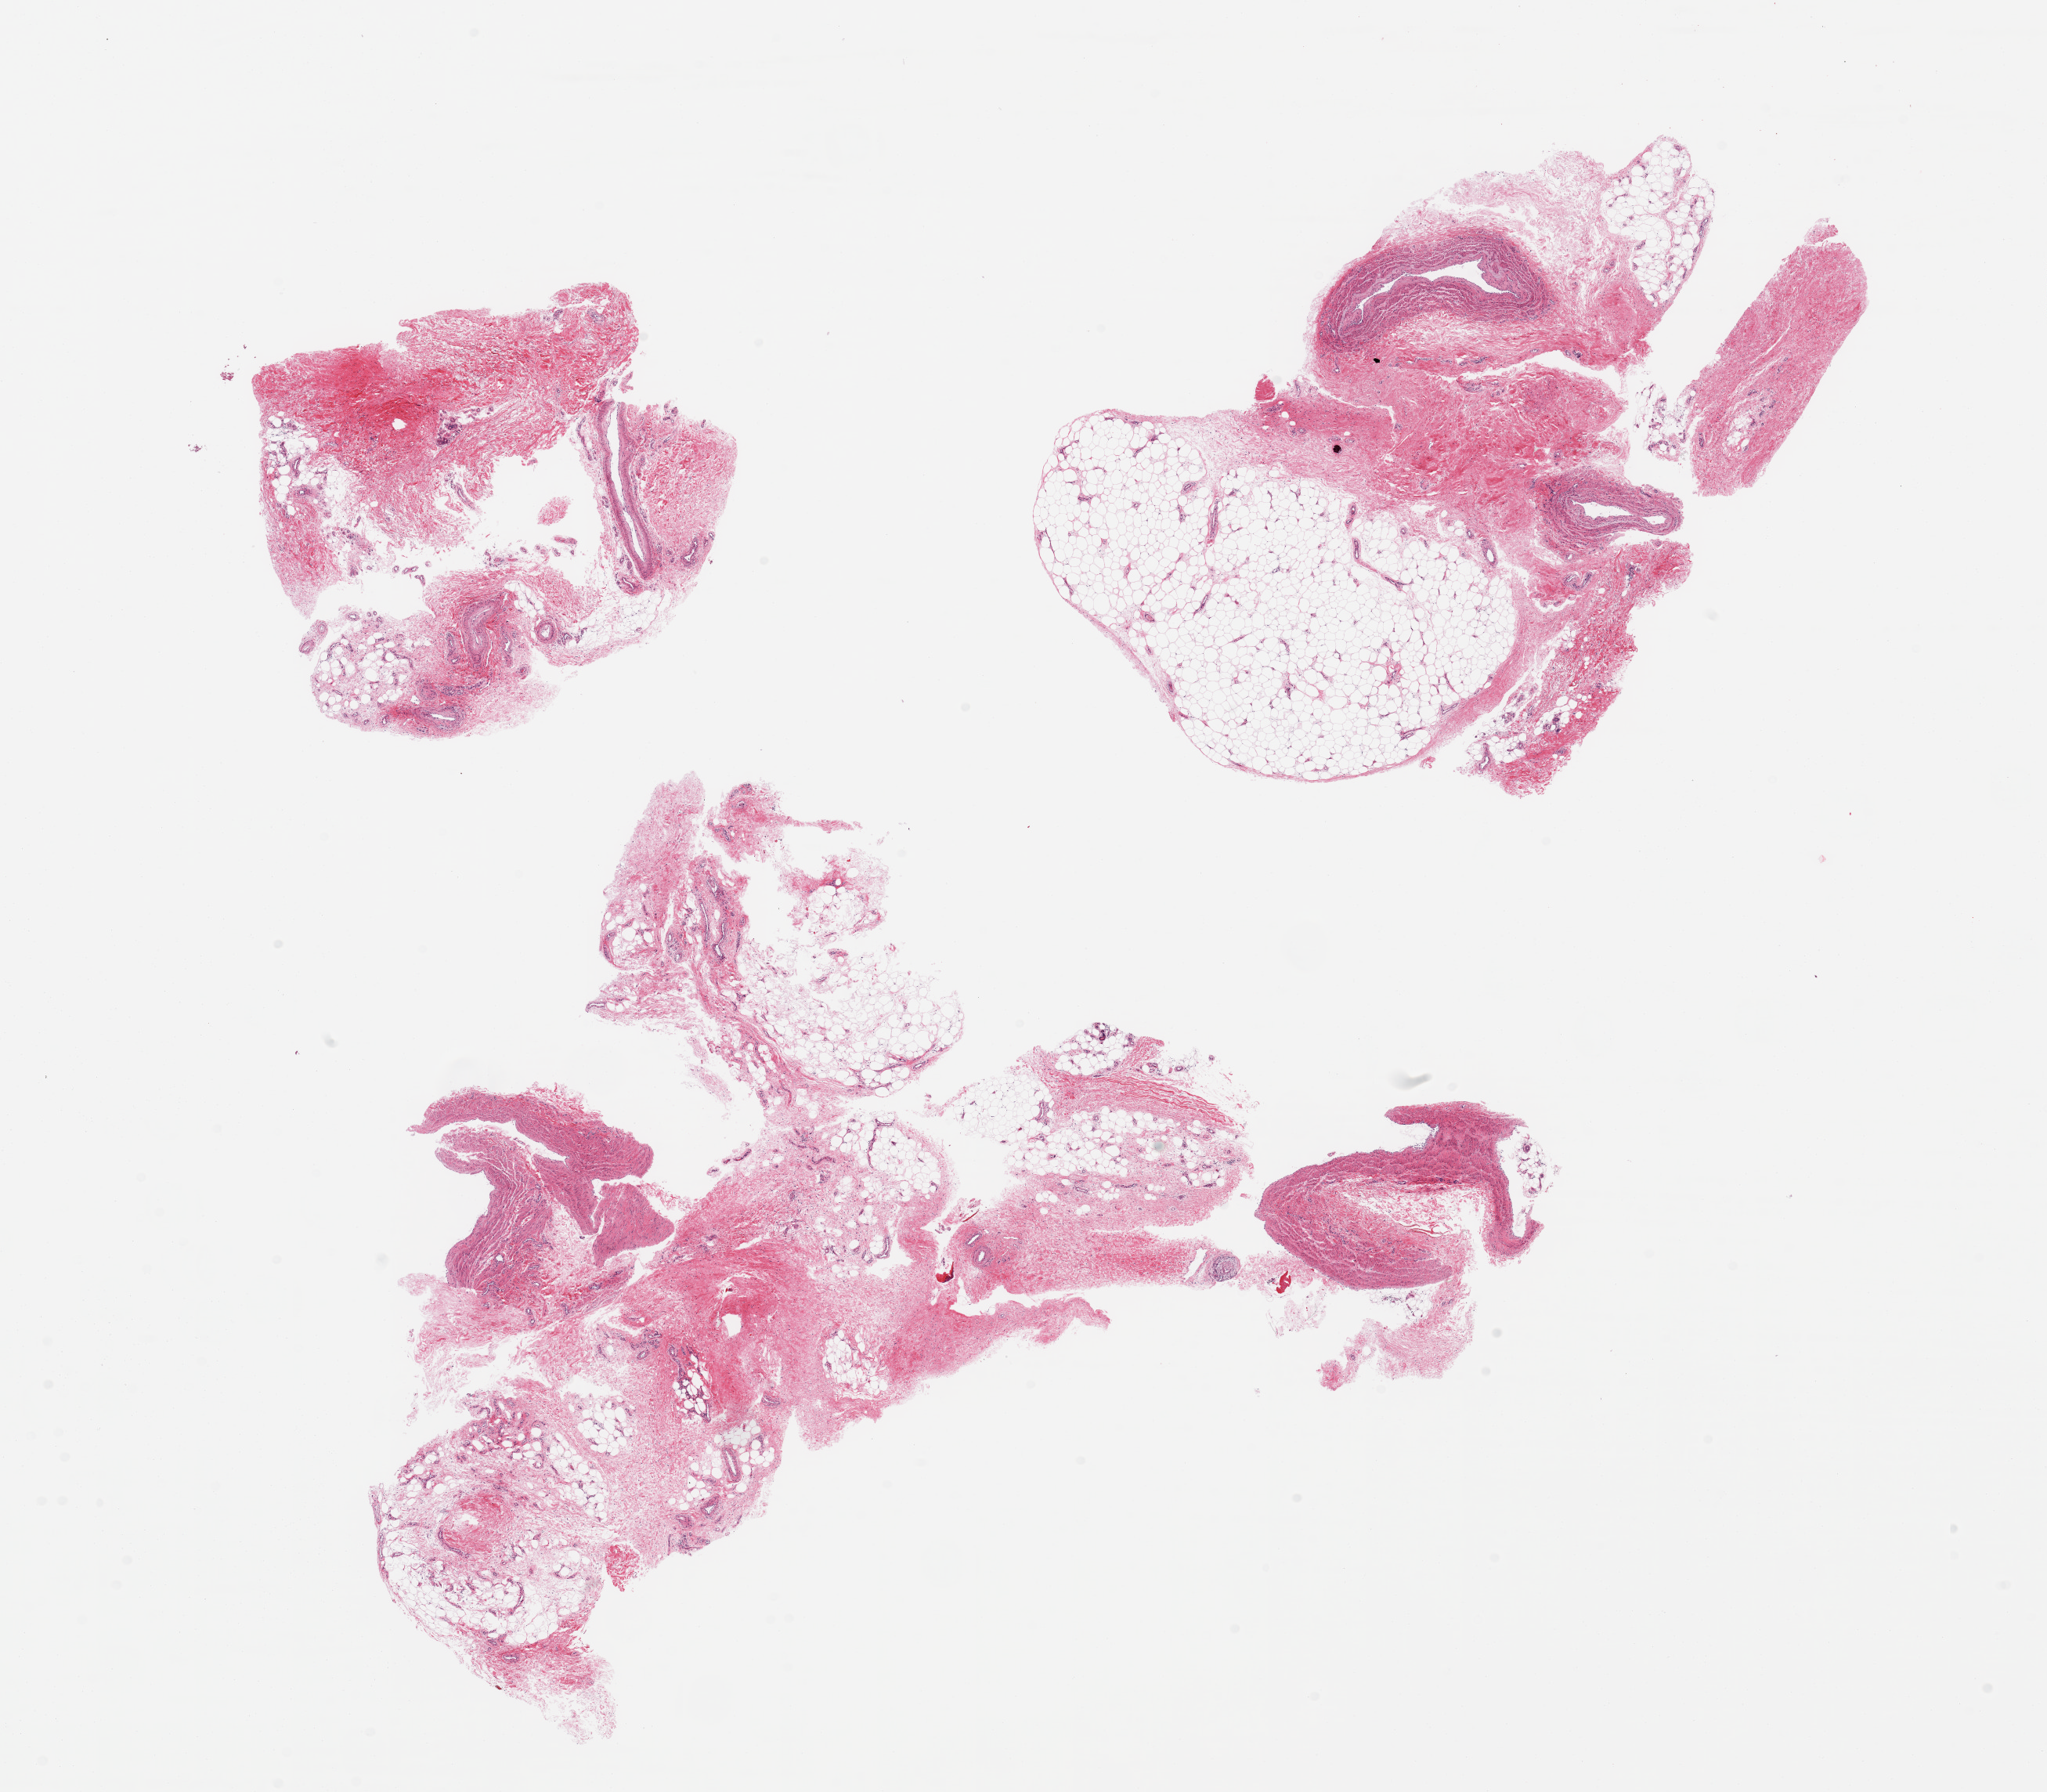
H&E whole-slide image — low-resolution overview of the scanned area, about 20.7 x 18.1 mm (slide scanned at 20x); PAXgene-fixed, paraffin-embedded tissue; target tissue: adipose tissue; donor tissue sample. Male donor.
Review note (as recorded): 3 pieces, ~25-30% fat, mainly fascia/vascular elements.